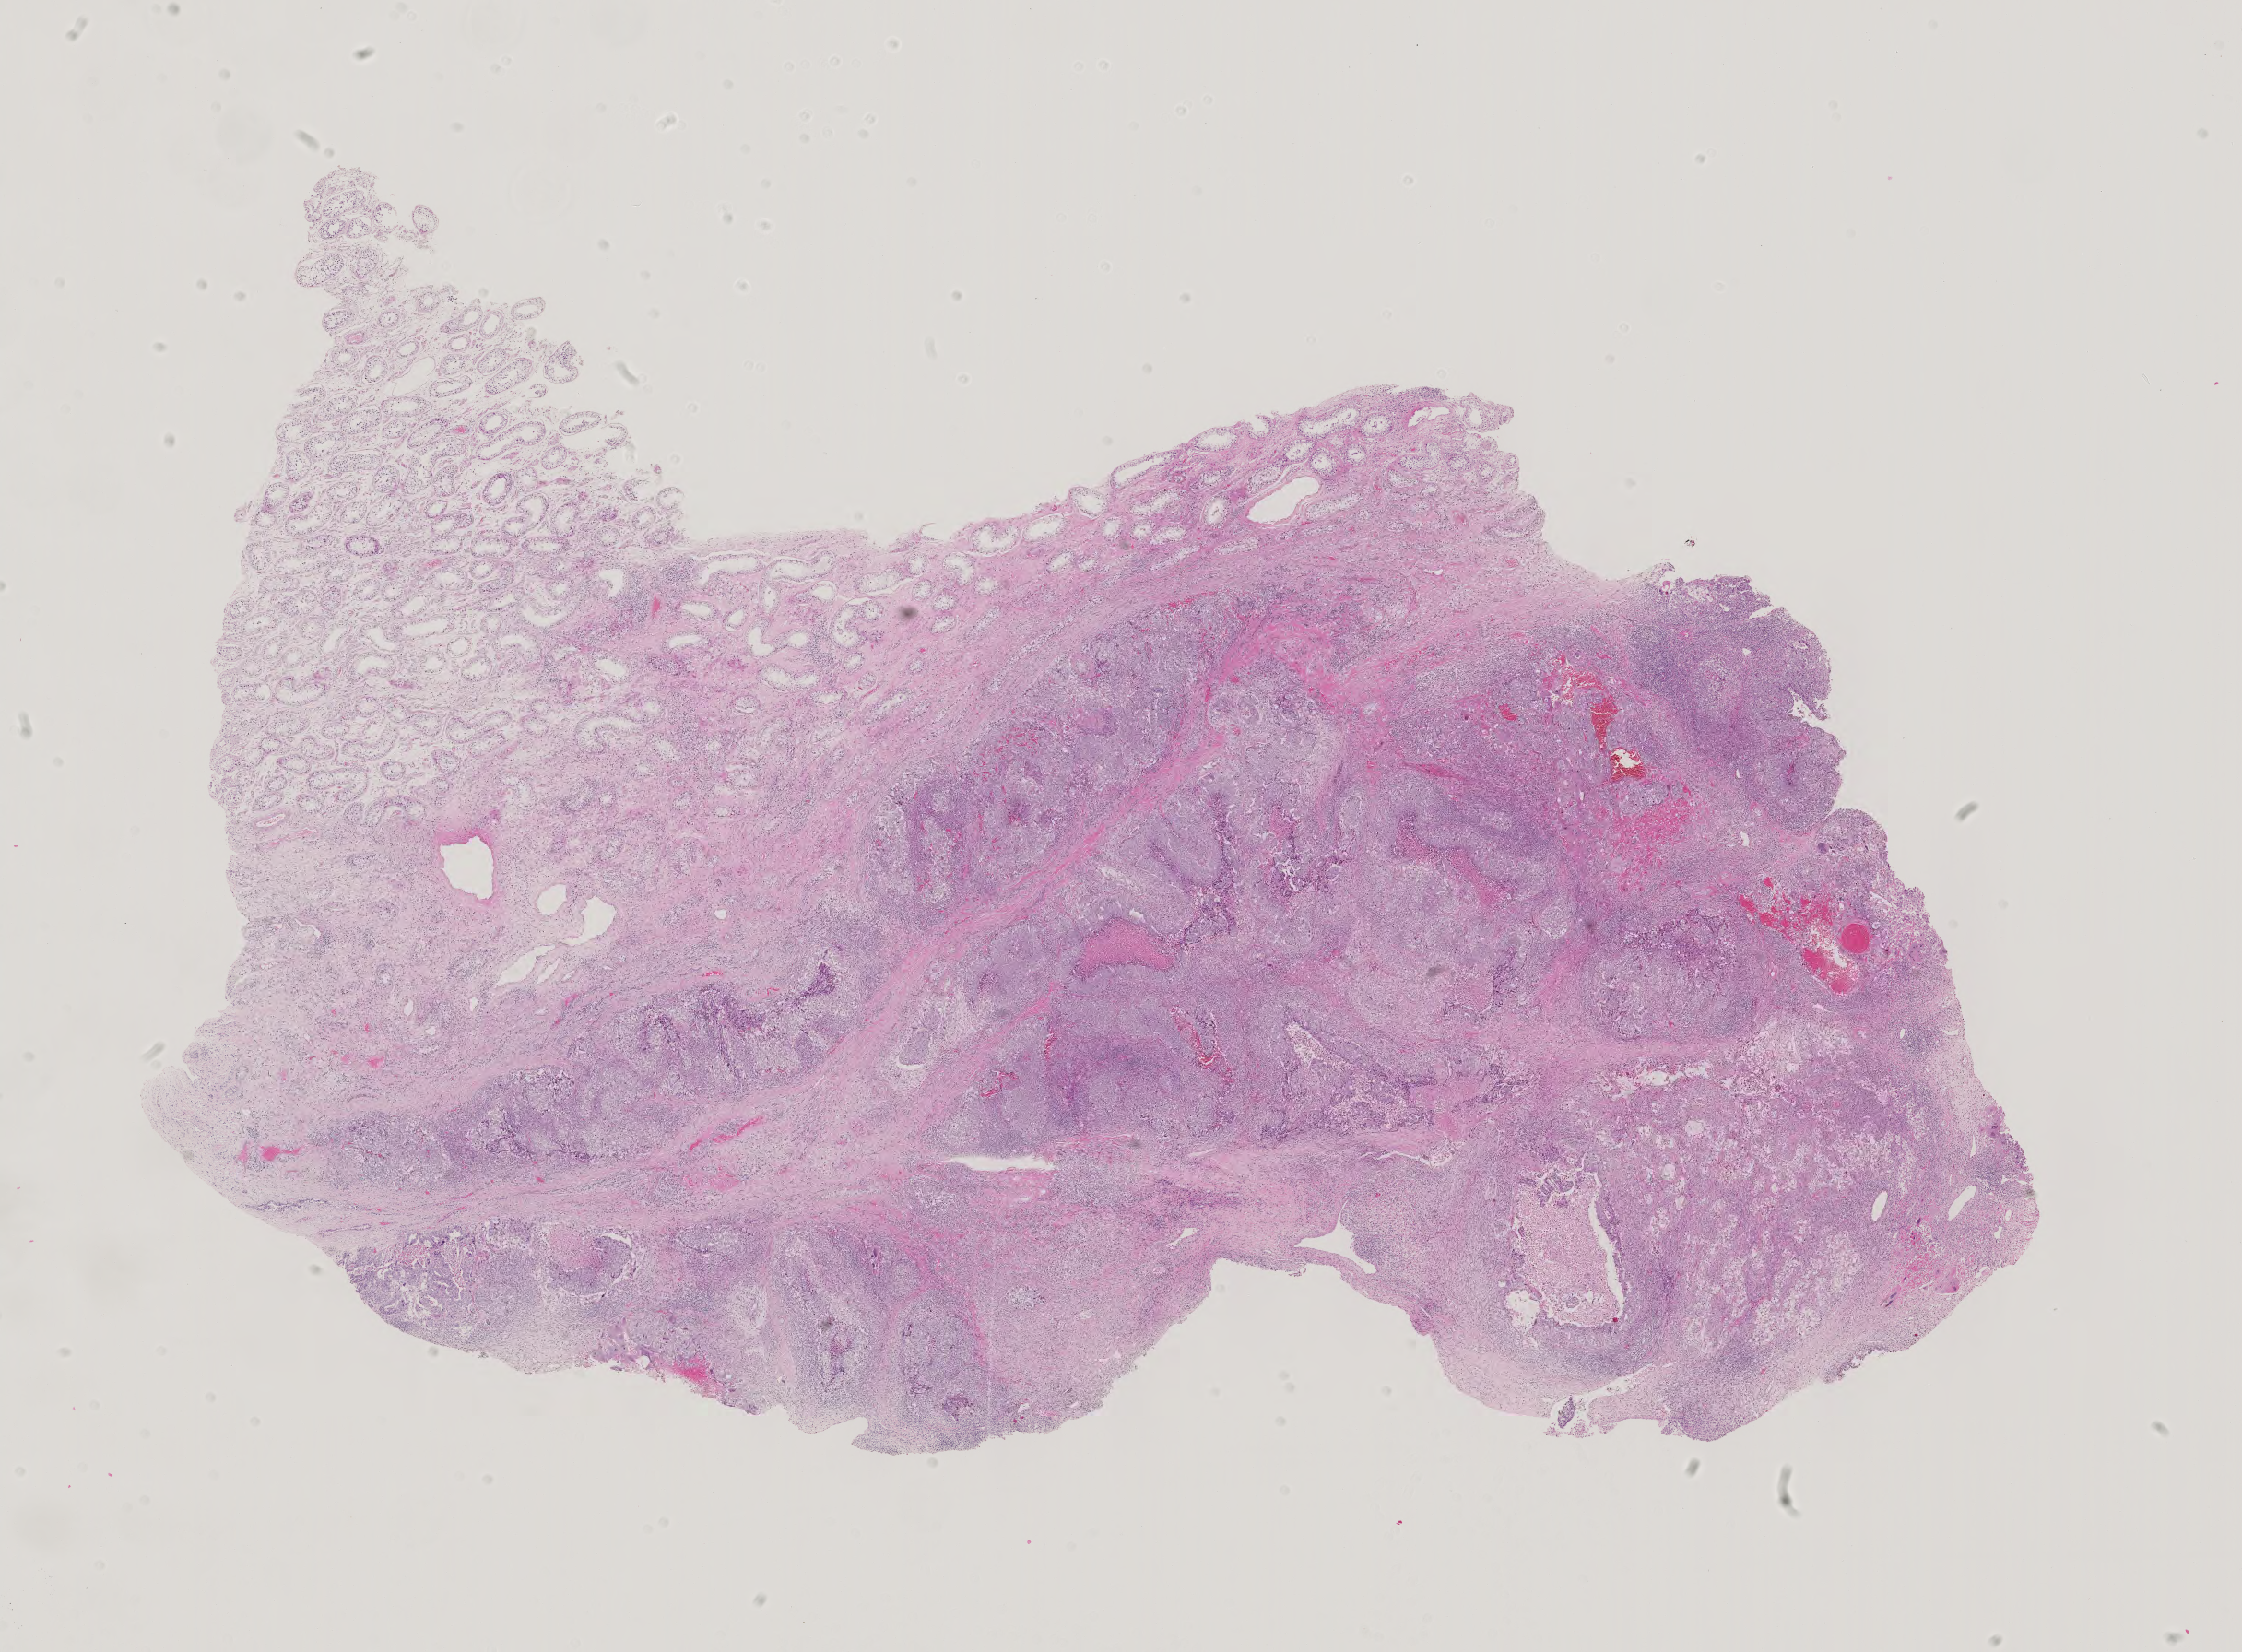
H&E-stained whole-slide image, a low-resolution overview of the entire scanned area, about 17.7 x 13.1 mm. Patient sex: male.
Specimen: formalin-fixed paraffin-embedded (FFPE) diagnostic section; testis, primary tumour sample.